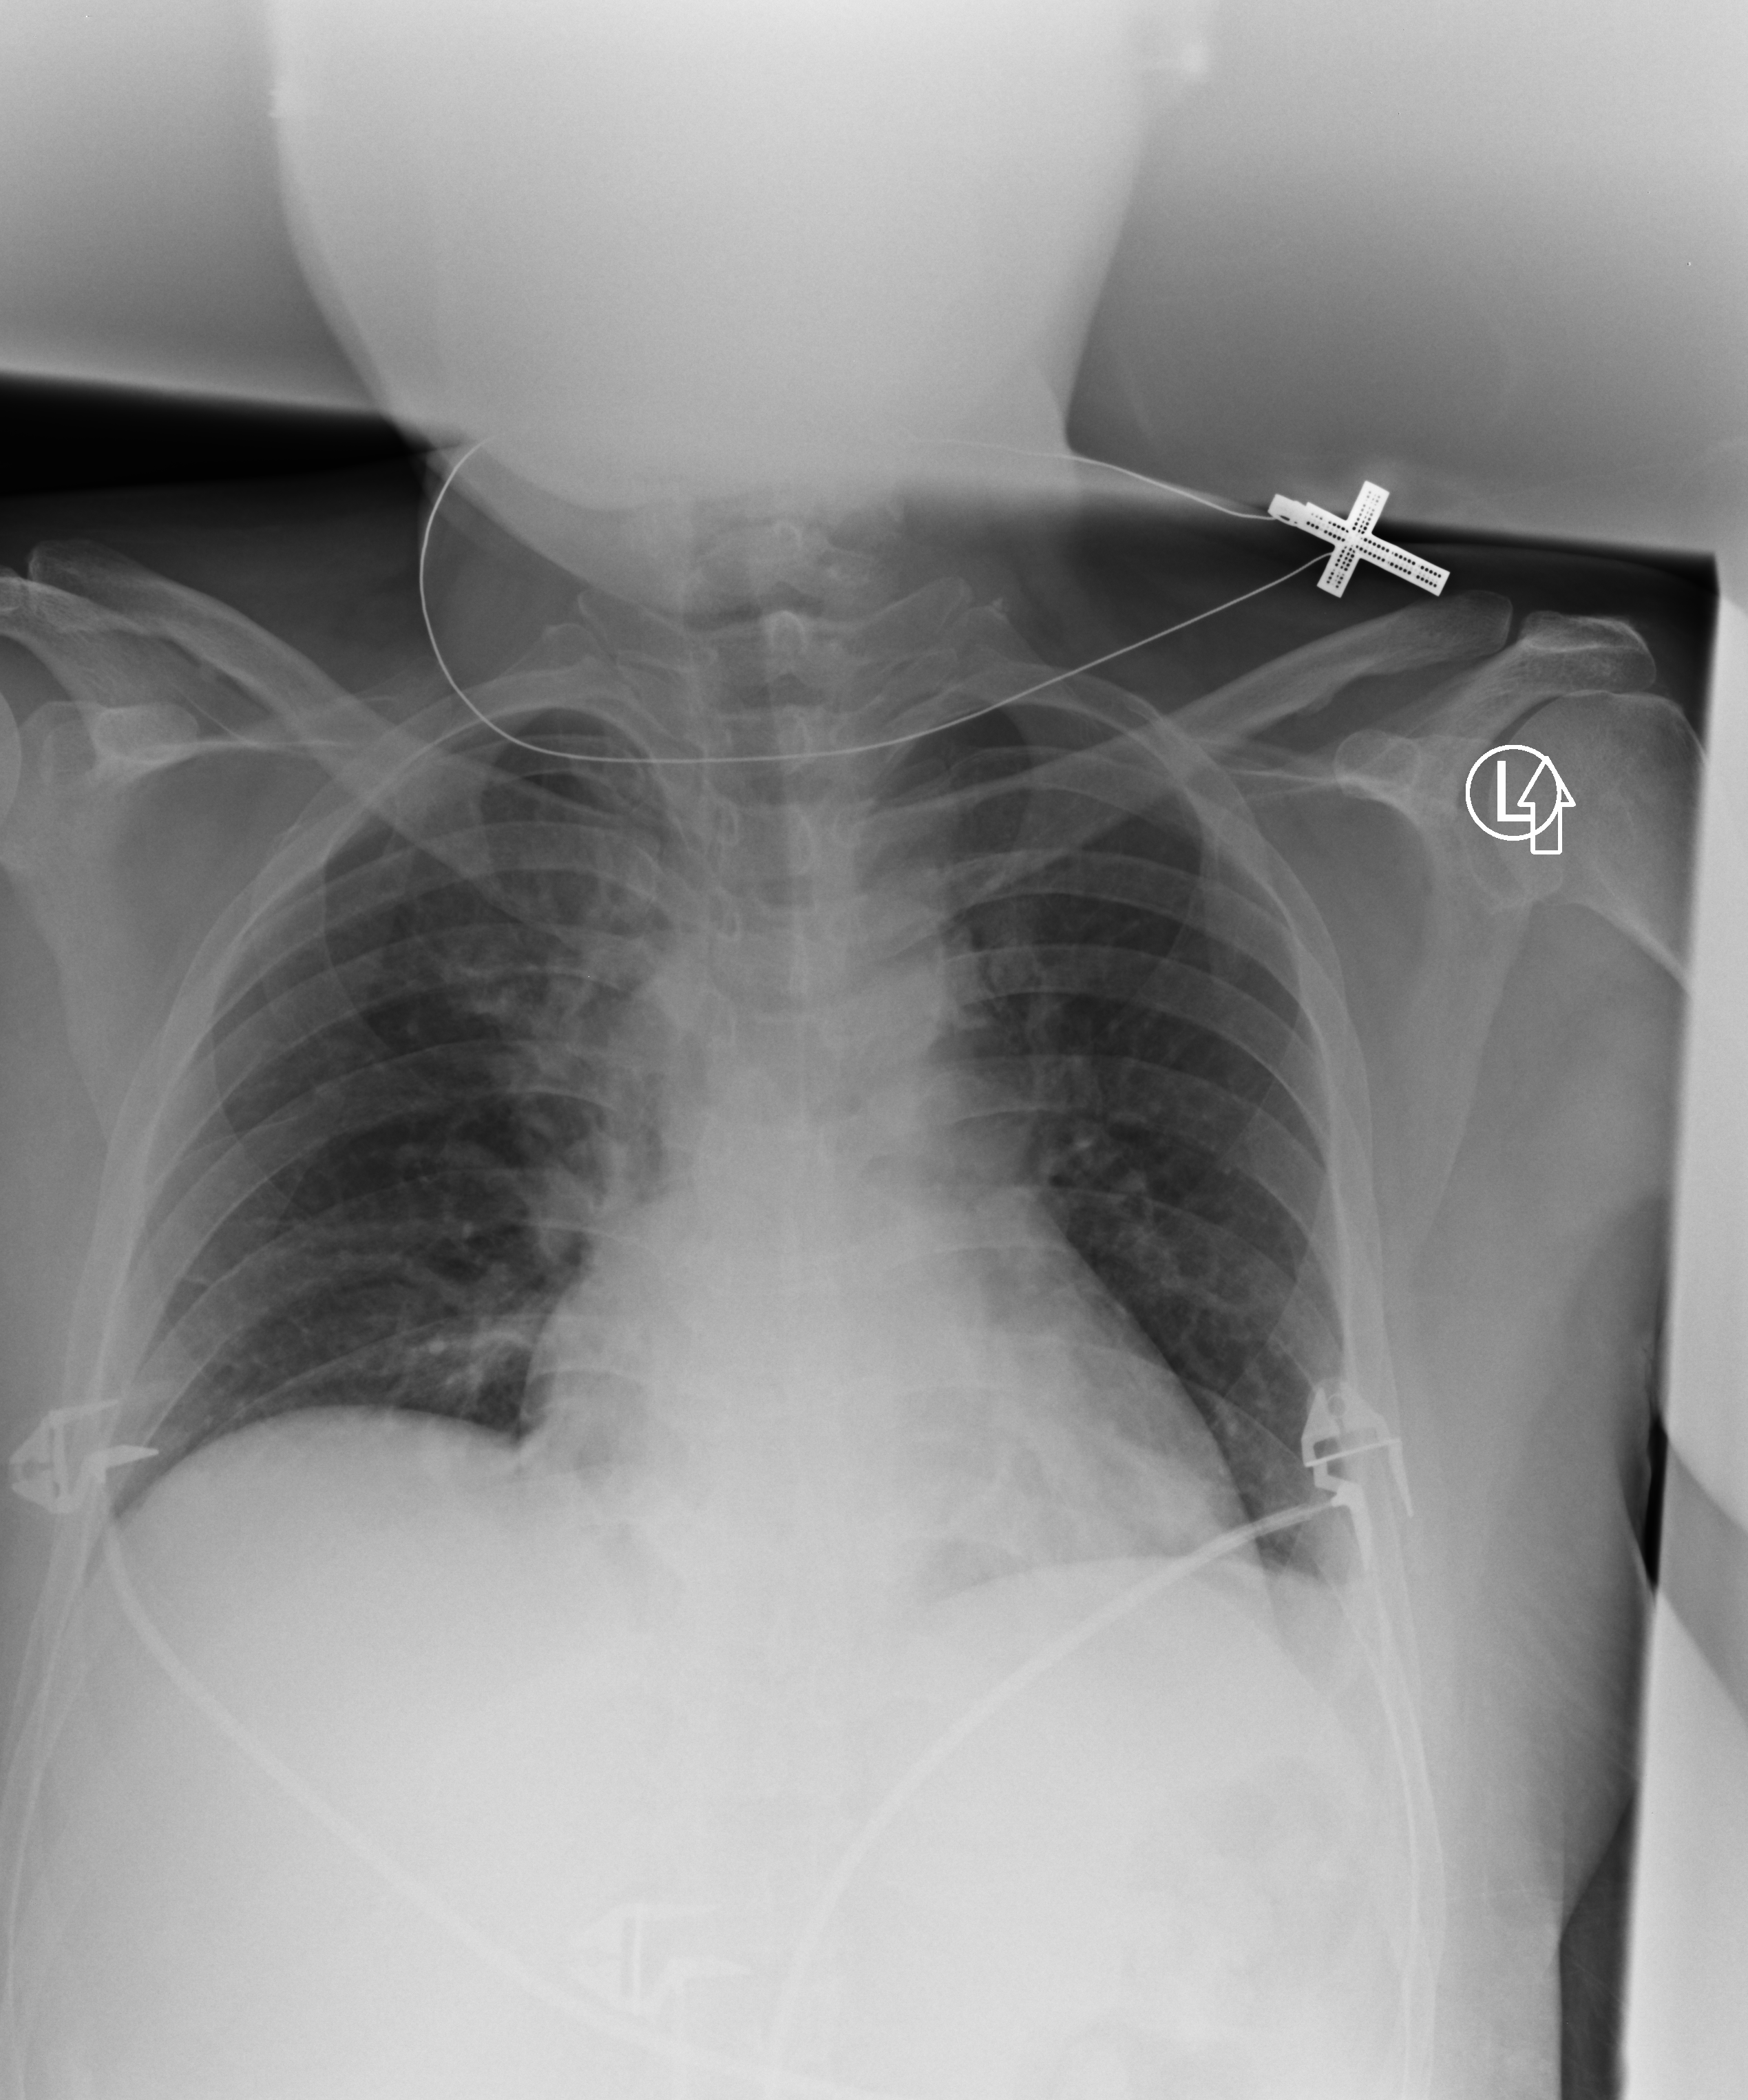
Chest X-ray (portable); anteroposterior (AP) projection. Female patient hospitalised with COVID-19, age 18–59 years.
Admission-level facts for this patient (not findings on this image; timing relative to this image not recorded): admitted to intensive care during this hospital stay: no; hypertension (admission record): yes; mechanically ventilated during this hospital stay: no.